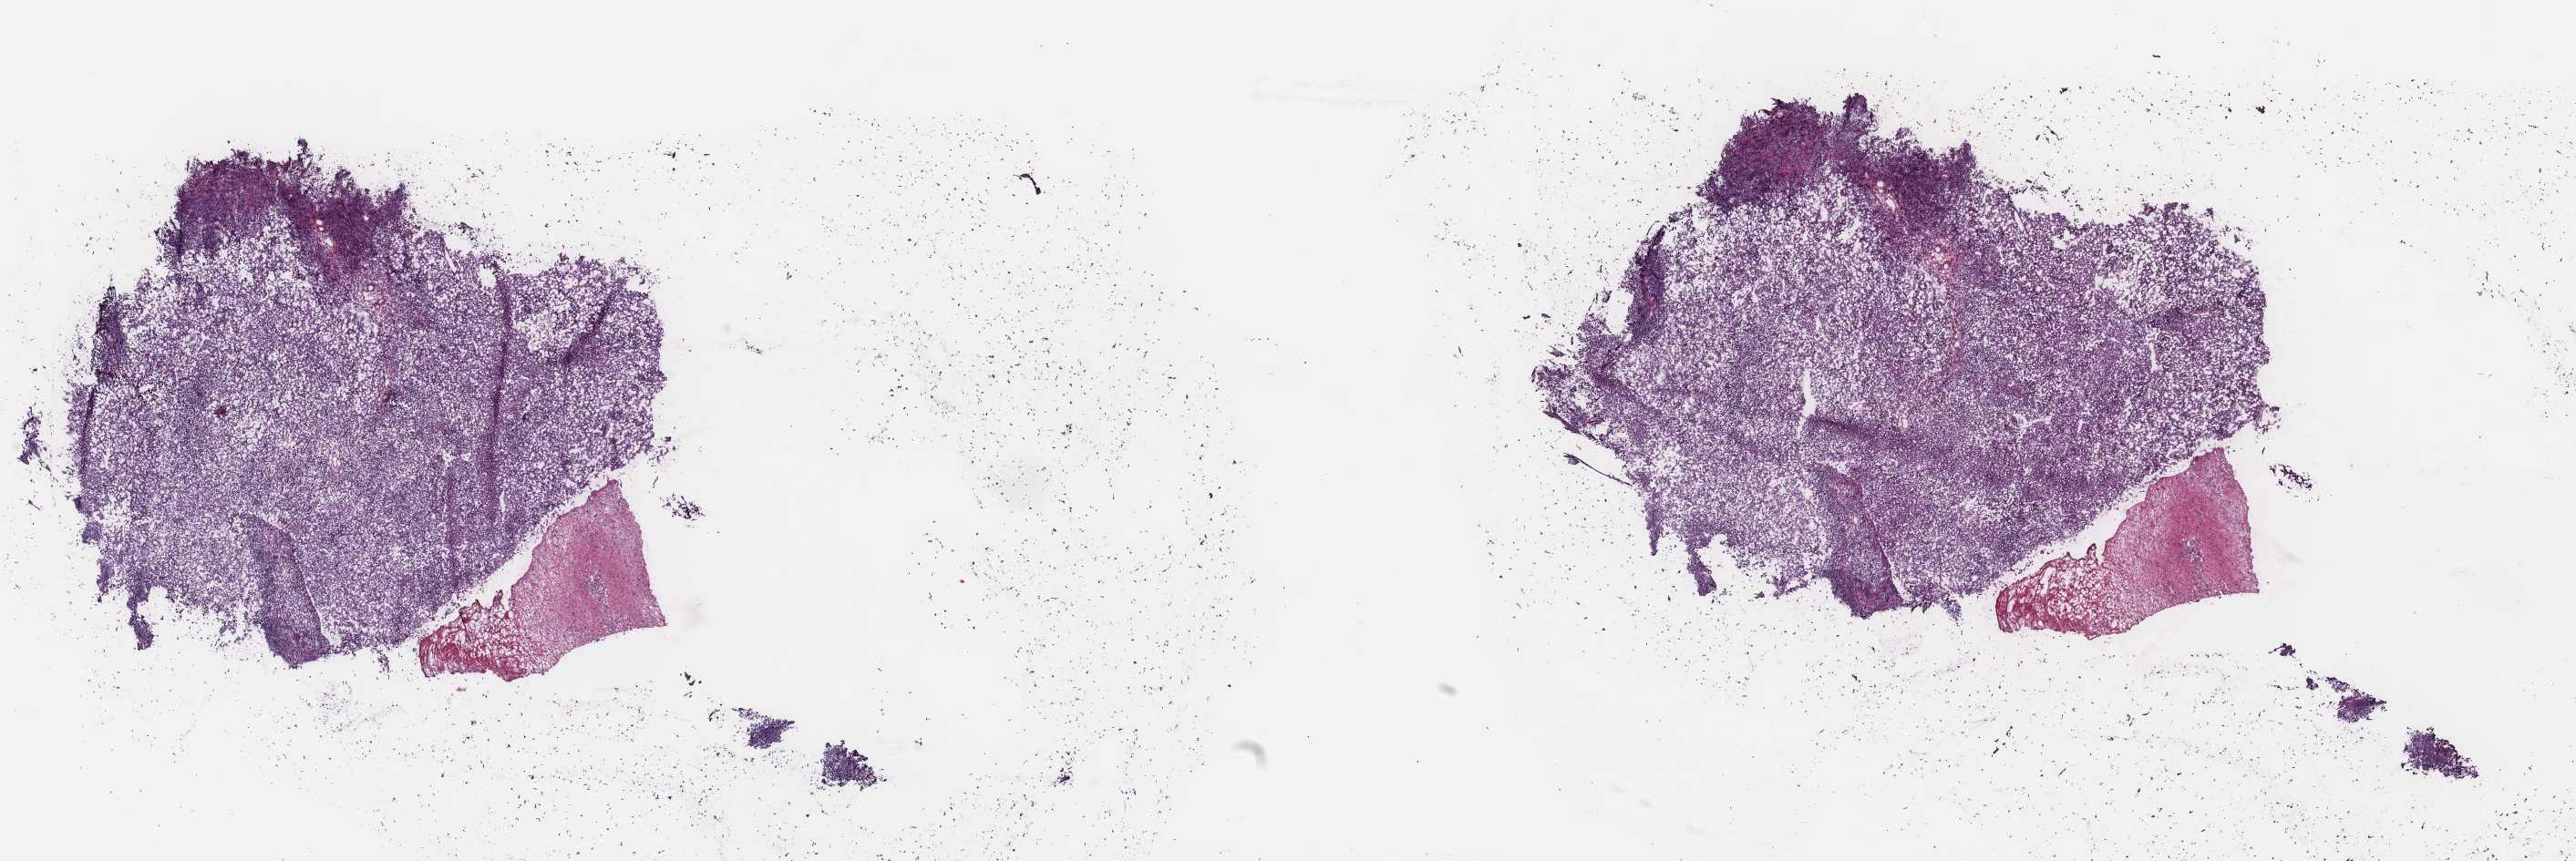
Digitized Hematoxylin and eosin (H&E) stained tissue section (whole slide) — shown as a low-resolution overview of the whole scanned area (about 22.4 x 7.5 mm); frozen section from the top of the tissue portion; metastatic tumour sample, sampled site: lymph nodes of inguinal region or leg. Patient: female, age at initial diagnosis 65 years. Pathologist review of this section (percent, as recorded): tumour cells 95%, tumour nuclei 90%, normal cells 0%, stromal cells 5%, necrosis 0%. Inflammatory infiltration, as recorded: lymphocyte infiltration 0%, monocyte infiltration 0%, neutrophil infiltration 0%.
This section: metastatic tumour tissue. Patient diagnosis: Malignant melanoma, NOS.